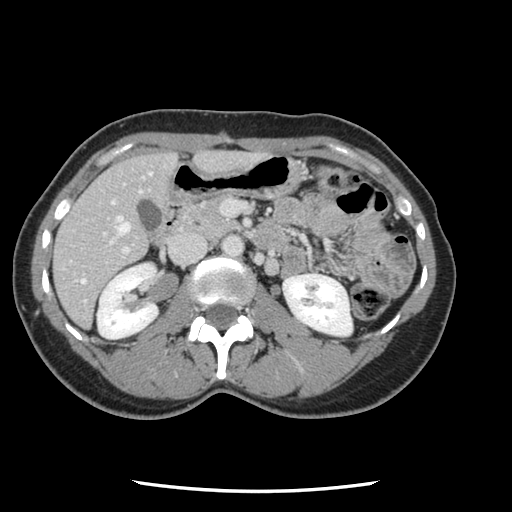
Contrast-enhanced abdominal CT, one axial slice. 120 kVp. Intravenous contrast given. Soft-tissue window (W 400 / L 40 HU). 2.5 mm slice thickness. 512 × 512 image matrix. Female patient, age 43 years. From the clinical record (not read from this slice): diagnosis: colorectal cancer liver metastases, imaged before liver resection; multiple liver metastases: yes; largest metastasis: 3.4 cm; disease in both lobes: yes.
Outlined on this slice (expert manual segmentation):
- hepatic veins: bounding box [x1, y1, x2, y2] px = [81, 173, 151, 283]
- liver: [55, 153, 252, 325]
- planned liver remnant (the part of the liver to remain after resection): [55, 154, 176, 326]
- portal vein (with intrahepatic branches): [69, 201, 246, 303]